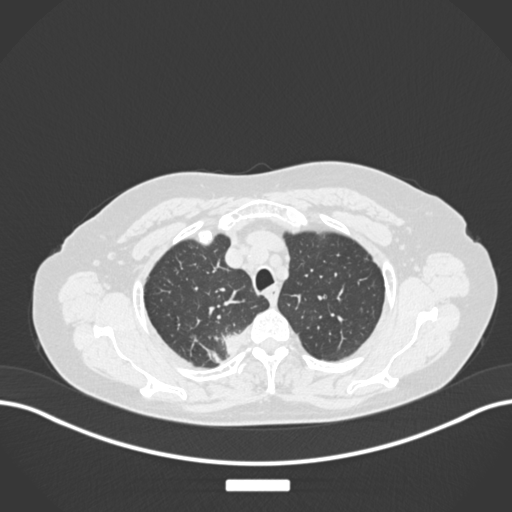
Chest CT, one axial slice; slice 213 of 237 in the series (ordered by position); 120 kVp; lung window (W 1500 / L -600 HU); 512 × 512 image matrix. Patient: female, 62 years. From the clinical record (not read from this slice): clinical TNM (as recorded): T1c N1 M0.
Structures marked on this image (rectangle marked by the reading radiologist):
- lung tumour (recorded histology: squamous cell carcinoma): bounding box [x1, y1, x2, y2] px = [218, 318, 255, 358]